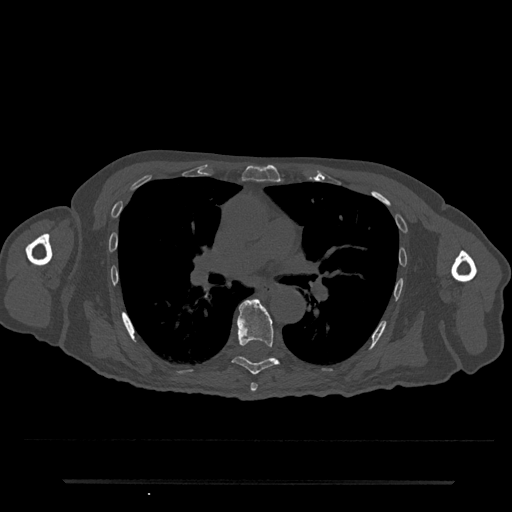
CT including the spine, one axial slice; slice 479 of 797 in the series (ordered by position); reconstruction kernel Br40s/3; bone window (W 1800 / L 400 HU); 0.5 mm slice thickness; 512 × 512 image matrix, field of view 427 × 427 mm. Patient: male, 74 years. From the clinical record (not read from this slice): primary cancer: prostate.
Annotated regions visible in this slice (semi-automatic segmentation, software-assisted and operator-edited):
- T6 vertebra: bounding box (x1, y1, x2, y2) in pixels: (250, 383, 258, 392)
- T7 vertebra: (232, 299, 280, 375)